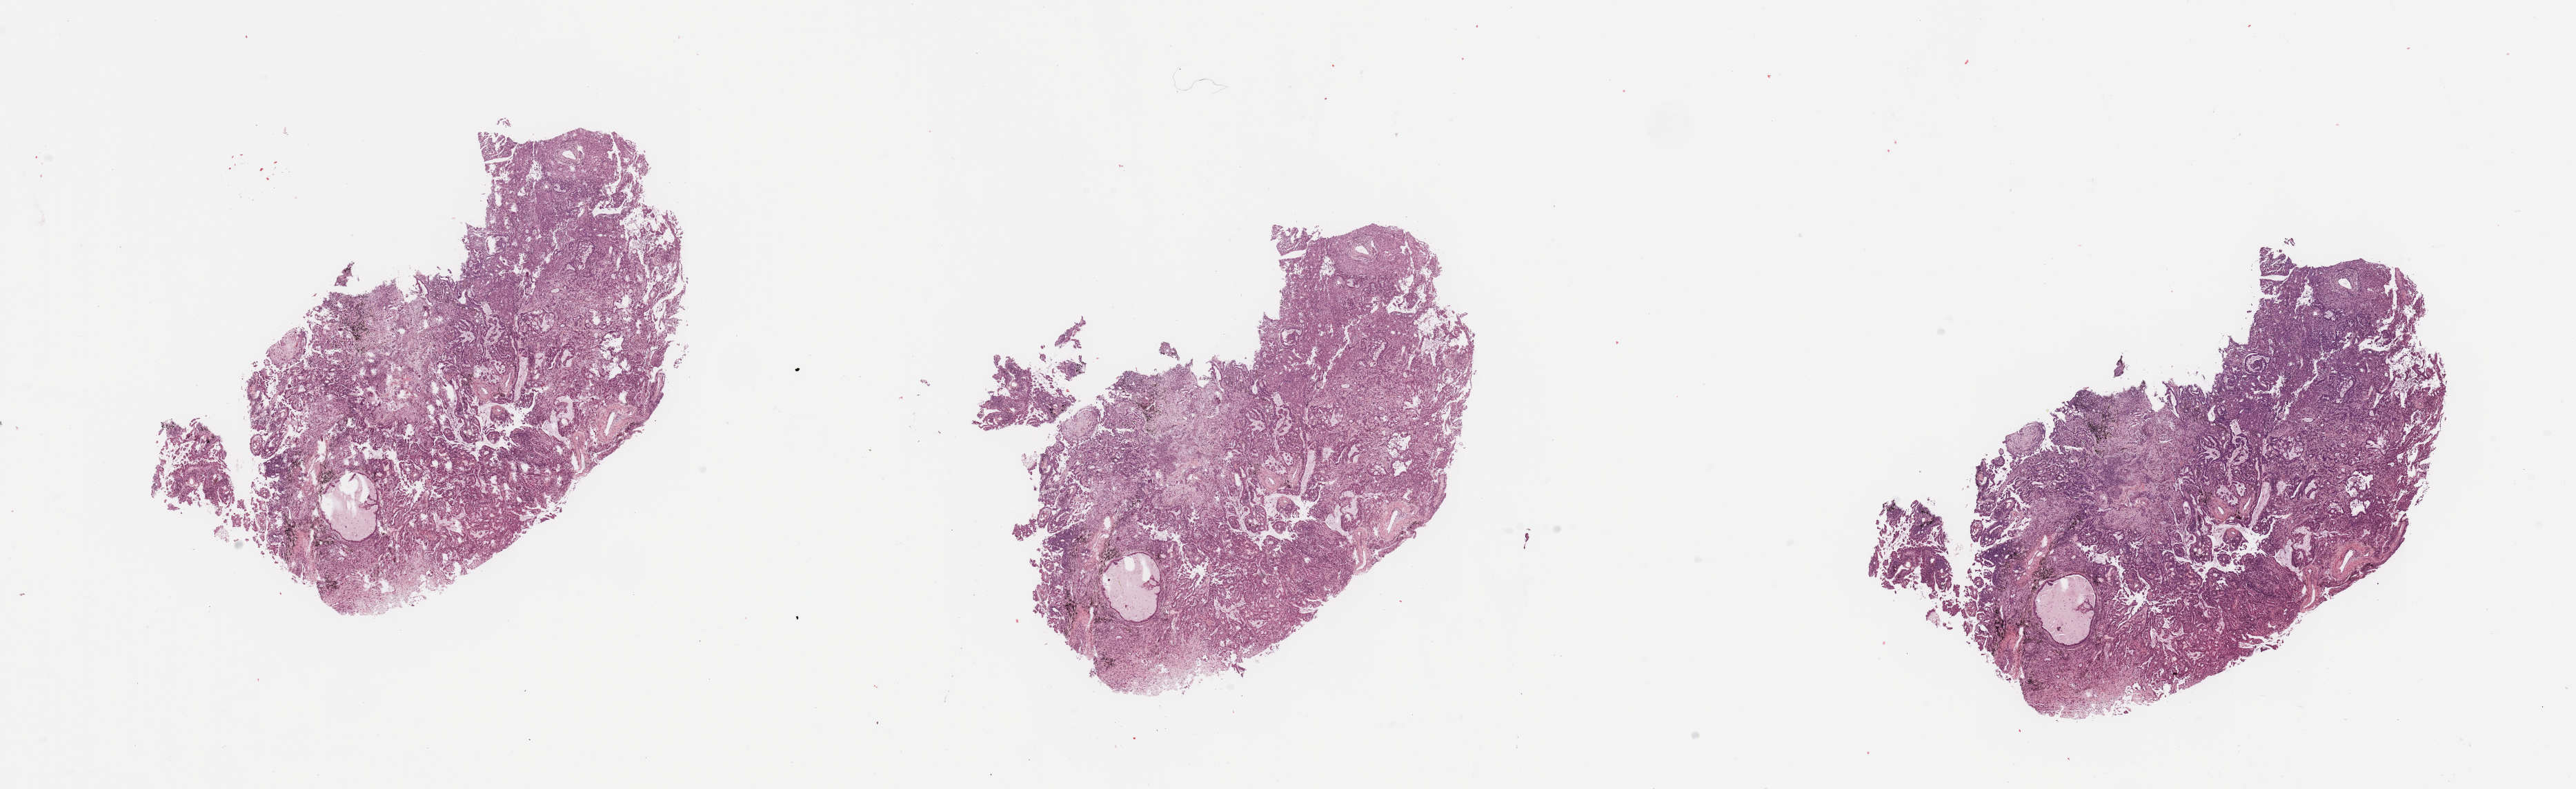
Whole-slide histology image, Hematoxylin and eosin (H&E) stained — shown as a low-resolution overview of the whole scanned area (about 29.5 x 9.0 mm, from a 20x scan); tumour tissue sample, sampled site: lung. Male, 69 y/o. Histologic grade: G3 (poorly differentiated). Composition of this section per pathologist review: tumour nuclei 70%, necrosis 5%.
* AJCC pathologic stage: IIB
* primary tumour site (as recorded): right upper lobe
* histologic diagnosis: Adenocarcinoma, NOS